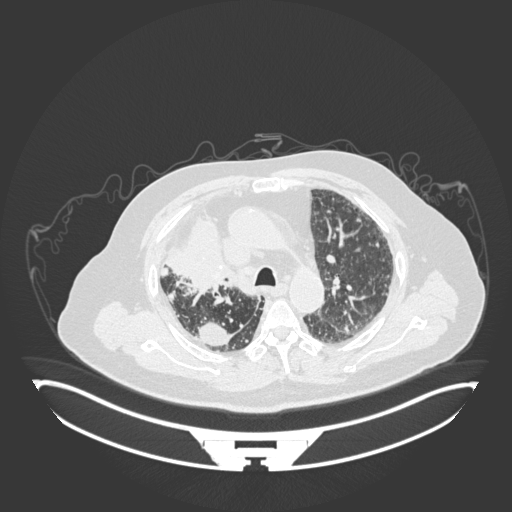
Chest CT, one axial slice. Position 126 of 201 along the scan axis. Lung window (W 1500 / L -600 HU). 512 × 512 image matrix, field of view 500 × 500 mm. Patient: male, 69 years. From the clinical record (not read from this slice): clinical TNM (as recorded): T4 N3 M1.
Outlined on this slice (rectangle marked by the reading radiologist):
- lung tumour (recorded histology: adenocarcinoma): box from (x=165, y=204) to (x=240, y=305) px